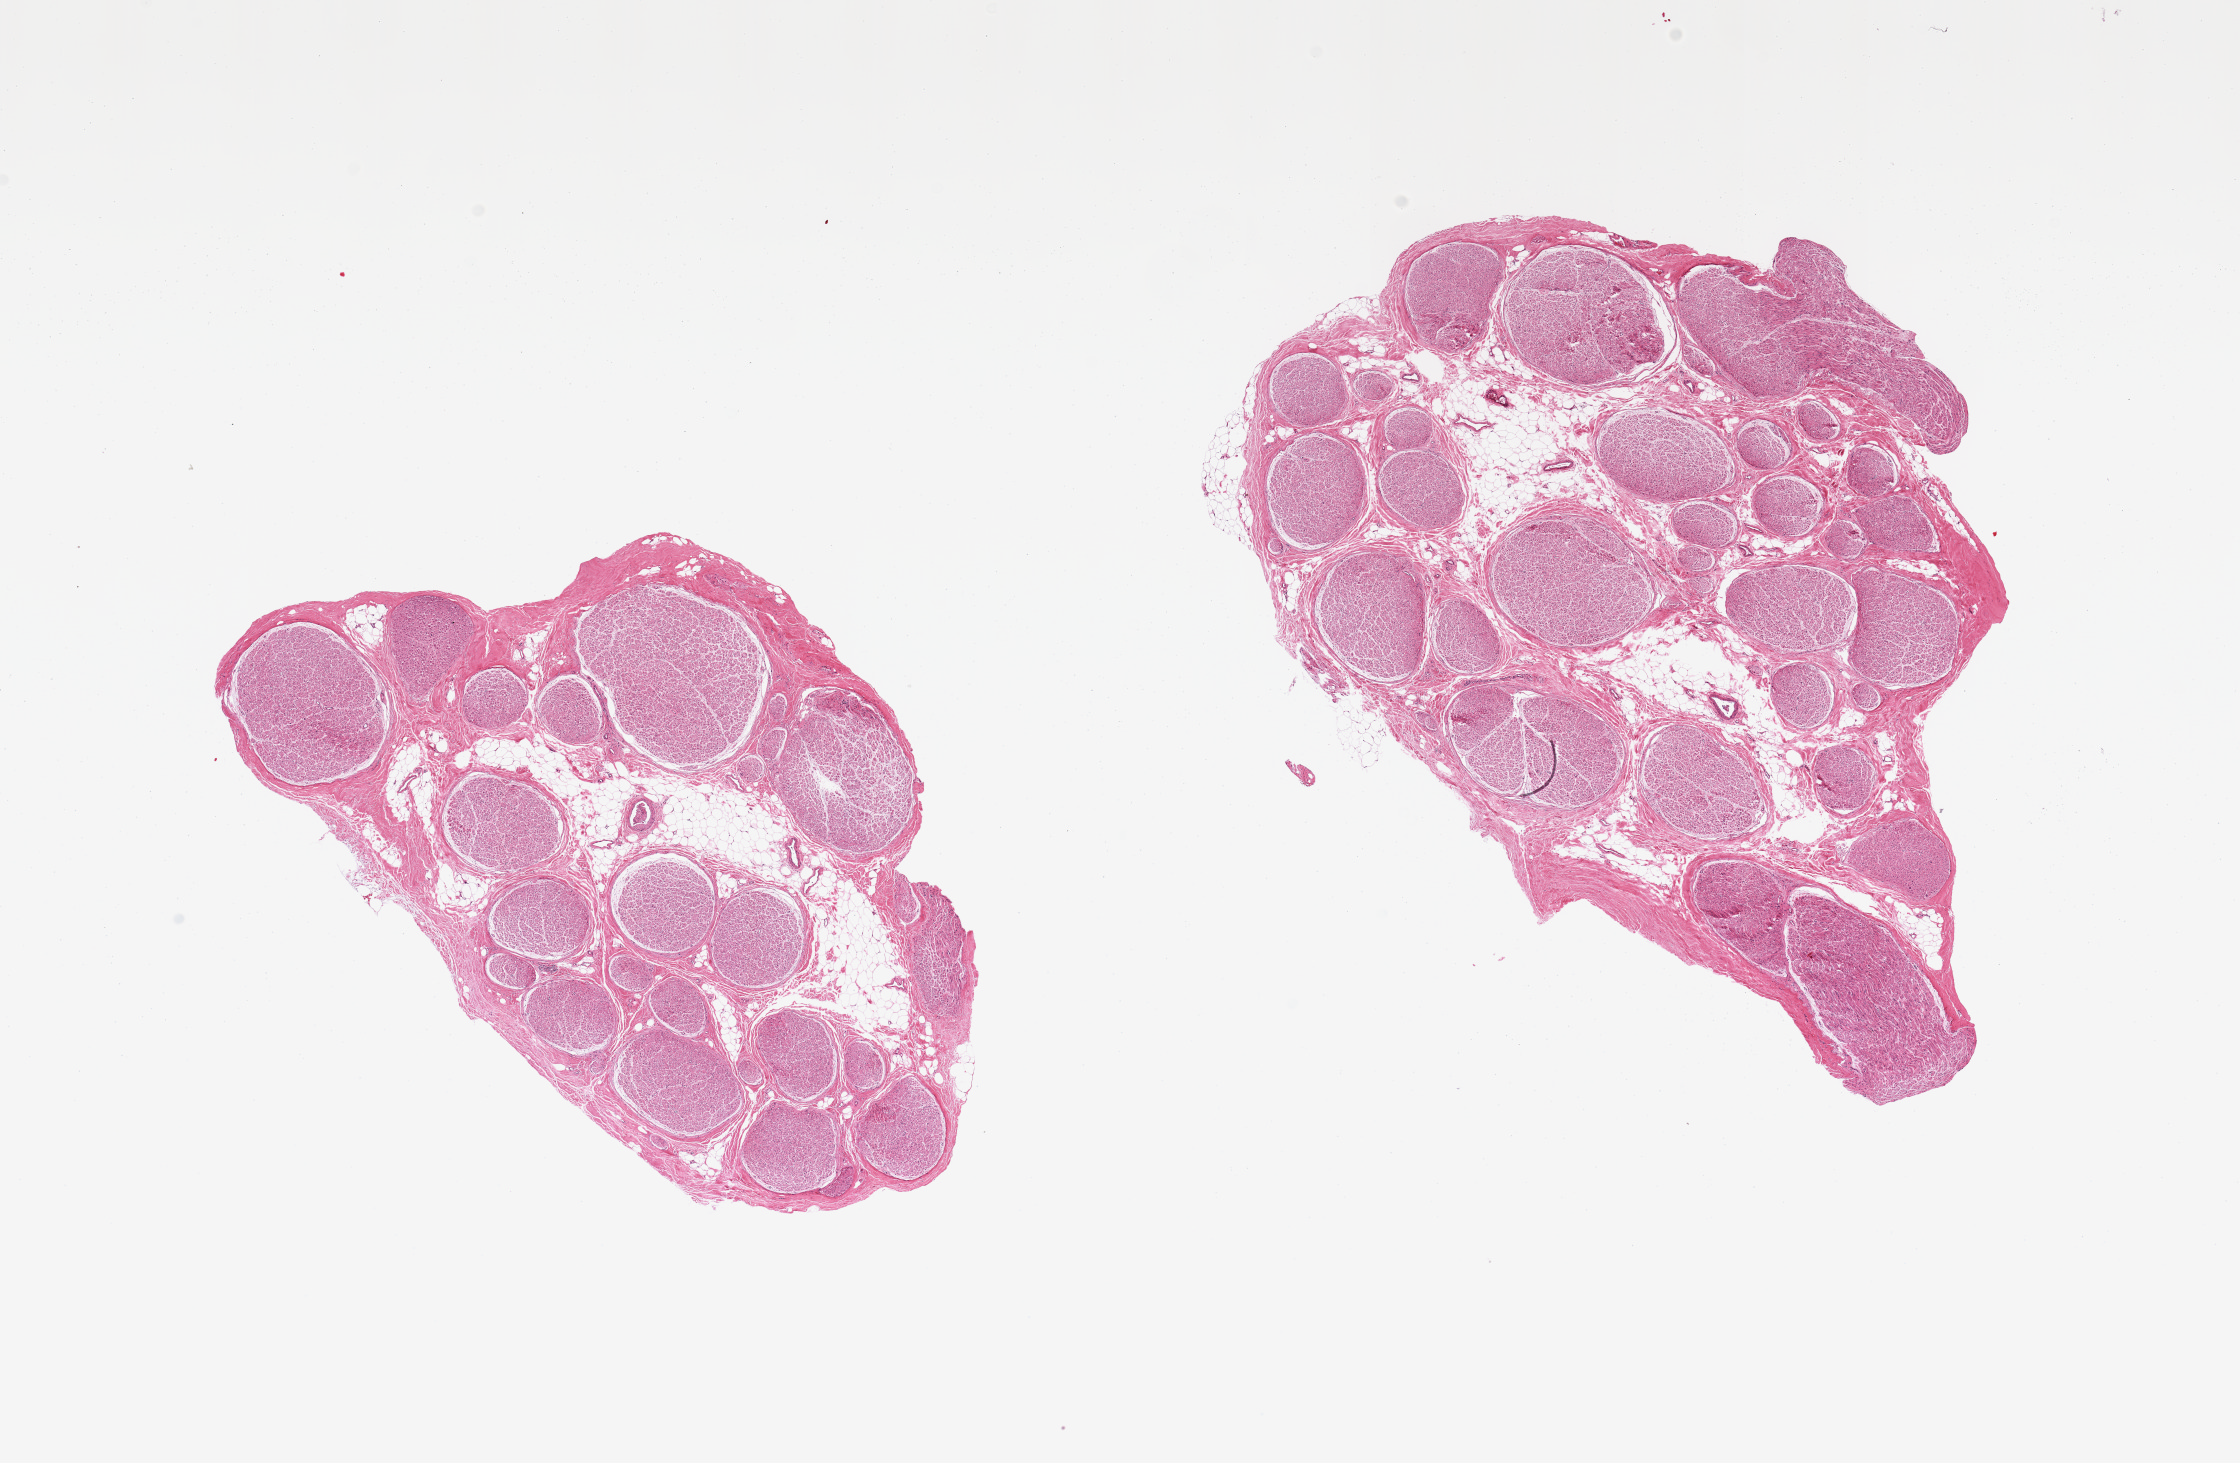
Digitized hematoxylin and eosin (H&E)-stained section, brightfield, whole scanned area (about 17.7 x 11.6 mm) shown as a low-resolution overview; PAXgene-fixed paraffin-embedded (PFPE) section; sampled site (target tissue): tibial nerve; donor tissue sample. Donor sex: female.
Review note (as recorded): 2 pieces, no significant adherent fat.